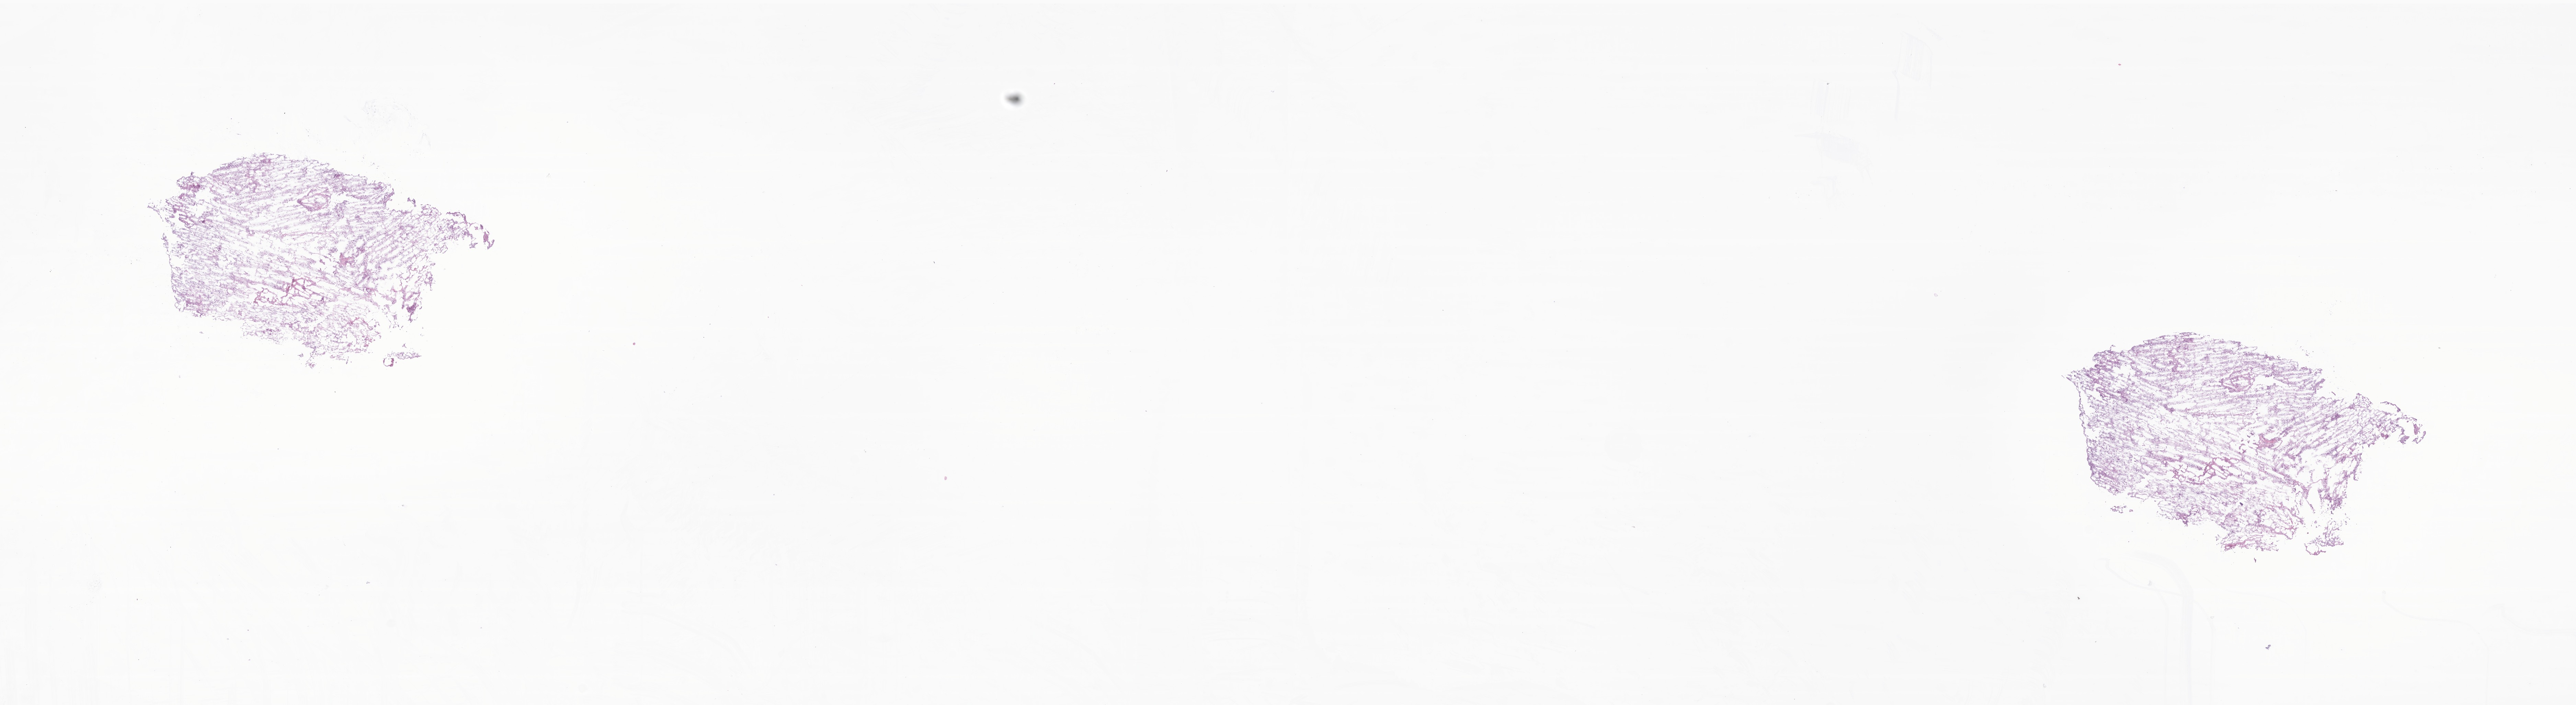
Digitized haematoxylin and eosin-stained section of tumor tissue from the brain — whole scanned area (about 31.6 x 8.7 mm) shown as a low-resolution overview, frozen section (OCT-embedded). Female patient, age 66 months (5 years 6 months).
- diagnosis (ICD-O-3 morphology term): Pilocytic astrocytoma